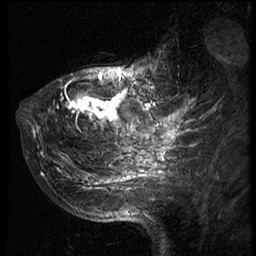
Breast MRI (dynamic contrast-enhanced), one sagittal slice; slice 22 of 66 in the series (ordered by position); 3 images stored at this slice position (order not interpretable as contrast timing); 1.5 T; TE 4.2 ms, TR 8.9 ms; 2.5 mm slice thickness; 256 × 256 image matrix, field of view 200 × 200 mm. Female patient, age 39 years. From the clinical record (not read from this slice): setting: breast cancer imaged before/during neoadjuvant chemotherapy; receptor status: HER2-positive.
Annotated regions visible in this slice (semi-automatically segmented with operator editing):
- analysis volume of interest (the breast-tissue region the enhancement analysis was run in; not a lesion): bounding box (x1, y1, x2, y2) in pixels: (29, 44, 166, 196)
- tumour enhancement mask (voxels above the 140 % enhancement threshold inside the analysis volume of interest): (32, 72, 164, 189)